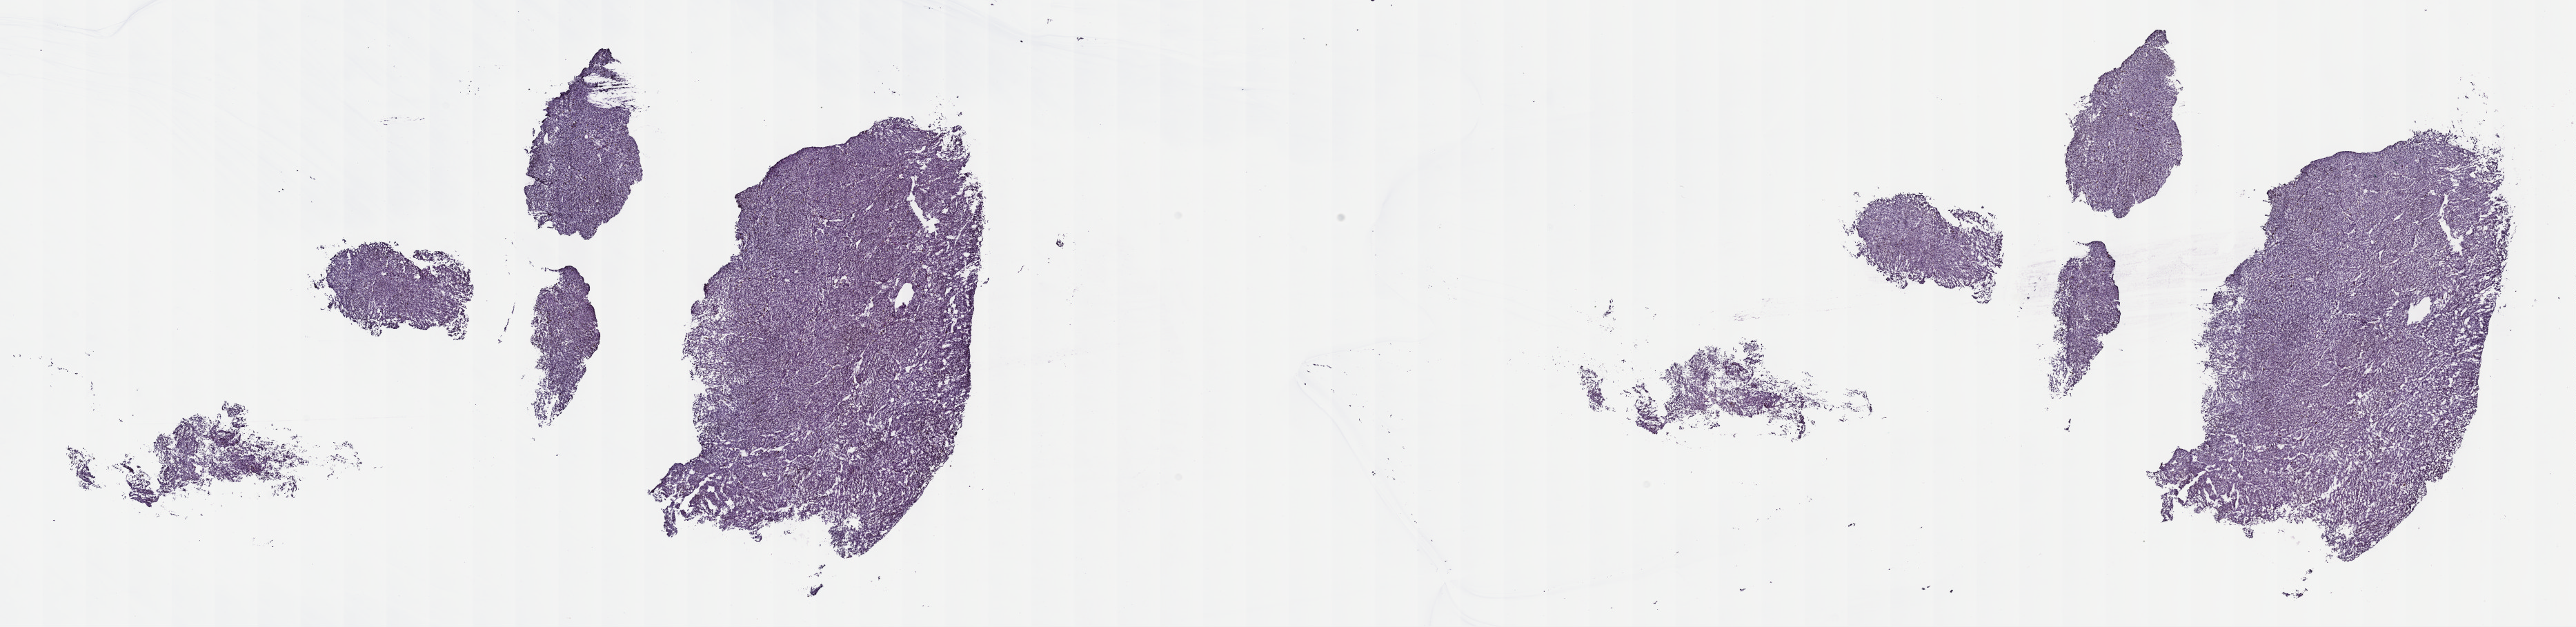
Whole-slide histology image, H&E, low-resolution overview of the scanned area, about 30.2 x 7.4 mm; frozen section from the top of the tissue portion; sample: primary tumour, uvea. Female, age 85 years at initial diagnosis. Composition of this section per pathologist review: tumour cells 98%, tumour nuclei 96%, normal cells 0%, stromal cells 0%, necrosis 2%. Infiltration values recorded for this section: lymphocyte infiltration 3%, monocyte infiltration 0%, neutrophil infiltration 0%.
* diagnosis: Mixed epithelioid and spindle cell melanoma (choroid)
* AJCC pathologic stage: IV (7th edition)